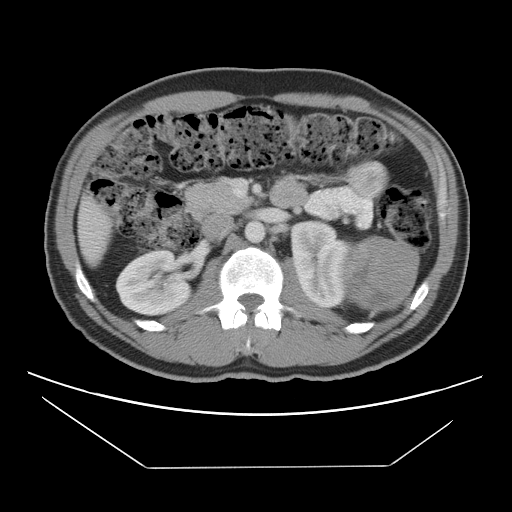
Contrast-enhanced abdominal CT, one axial slice; position 63 of 131 along the scan axis; reconstruction kernel STANDARD; intravenous contrast given; soft-tissue window (W 400 / L 40 HU); 5 mm slice thickness; 512 × 512 image matrix, field of view 396 × 396 mm. Patient: male, 44 years. Case-level facts recorded for this patient, not image findings: diagnosis: adrenocortical carcinoma; tumour side: left adrenal; tumour size at pathology: 15.5 cm; Ki-67 index: 6 %; stage (as recorded): 2.
Annotated regions visible in this slice (semi-automatically segmented with operator editing):
- mass: bounding box (x1, y1, x2, y2) in pixels: (345, 236, 416, 308)